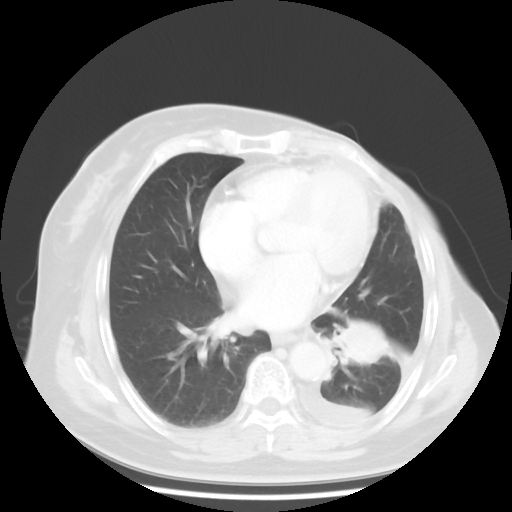
Chest CT, one axial slice; slice 19 of 48 in the series (ordered by position); reconstruction kernel STANDARD; 120 kVp; lung window (W 1500 / L -600 HU); 5 mm slice thickness; 512 × 512 image matrix, field of view 360 × 360 mm. Female patient, age 63 years. From the clinical record (not read from this slice): clinical TNM (as recorded): T2 N0 M1.
Structures marked on this image (rectangle marked by the reading radiologist):
- lung tumour (recorded histology: adenocarcinoma): bounding box <324,315,404,383> (left, top, right, bottom; pixels)